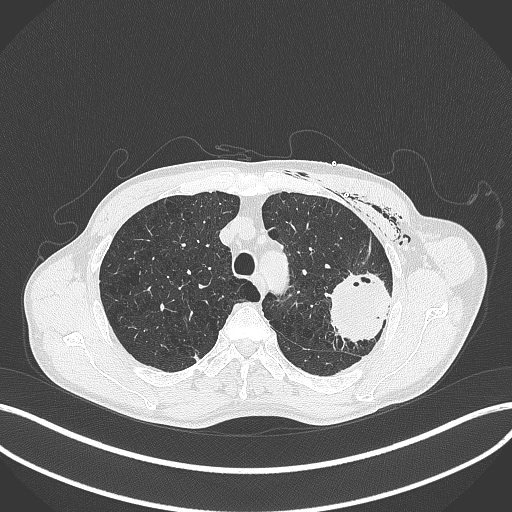
Chest CT, one axial slice. Slice 314 of 457 in the series (ordered by position). Reconstruction kernel B70f. 120 kVp. Lung window (W 1500 / L -600 HU). 1 mm slice thickness. 512 × 512 image matrix, field of view 400 × 400 mm. Patient: male, 58 years. Case-level facts recorded for this patient, not image findings: clinical TNM (as recorded): T3 N0 M0.
Outlined on this slice (rectangle marked by the reading radiologist):
- lung tumour (recorded histology: adenocarcinoma): bounding box <323,268,395,346> (left, top, right, bottom; pixels)